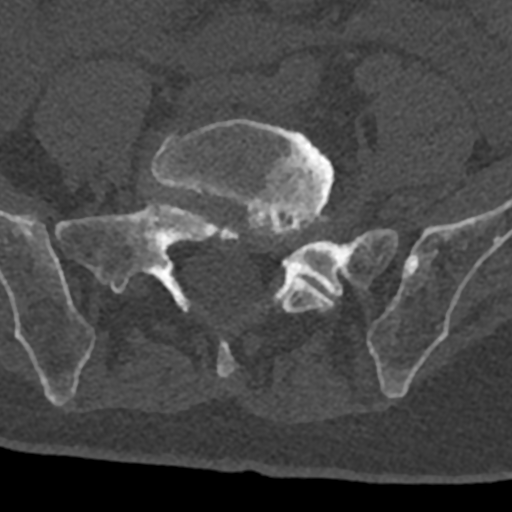
CT including the spine, one axial slice; reconstruction kernel Br40s/3; bone window (W 1800 / L 400 HU); 512 × 512 image matrix, field of view 160 × 160 mm. Patient: male, 74 years. Case-level facts recorded for this patient, not image findings: primary cancer: renal; vertebrae with lytic lesions (as recorded): T10, L1, L2, L3, L4, L5.
Annotated regions visible in this slice (semi-automatically segmented with operator editing):
- L5 vertebra: box from (x=151, y=118) to (x=347, y=379) px